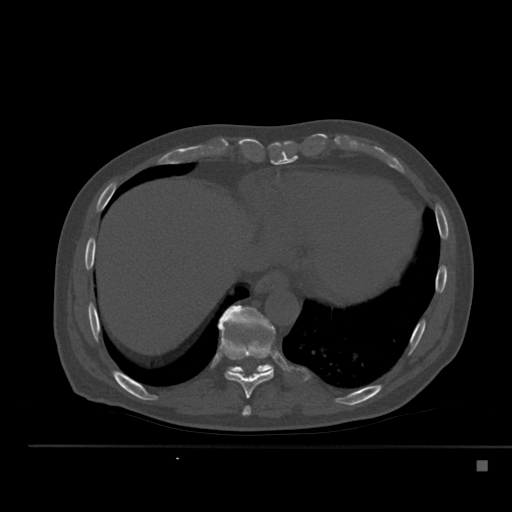
CT including the spine, one axial slice; position 283 of 517 along the scan axis; reconstruction kernel Br40s; bone window (W 1800 / L 400 HU); 1.5 mm slice thickness; 512 × 512 image matrix. Male patient, age 70 years. Case-level facts recorded for this patient, not image findings: primary cancer: renal; vertebrae with lytic lesions (as recorded): T4, T6, T10, T12, L3, L4, L5.
Outlined on this slice (semi-automatically segmented with operator editing):
- T10 vertebra: bounding box <218,305,275,374> (left, top, right, bottom; pixels)
- T8 vertebra: <242,406,251,416>
- T9 vertebra: <218,321,274,398>